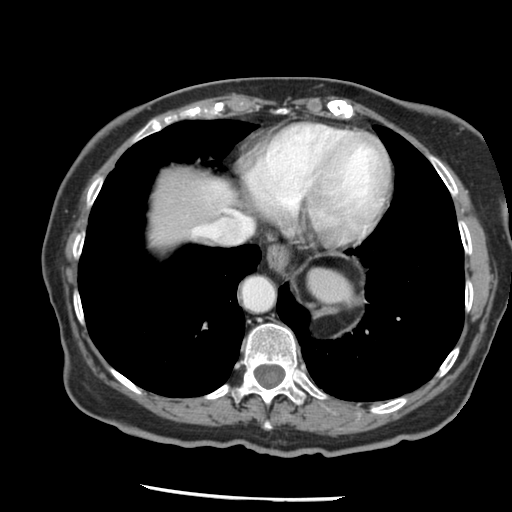
Contrast-enhanced abdominal CT, one axial slice; position 119 of 148 along the scan axis; soft-tissue window (W 400 / L 40 HU); 2.5 mm slice thickness; 512 × 512 image matrix, field of view 330 × 330 mm. Female patient, age 85 years. From the clinical record (not read from this slice): diagnosis: colorectal cancer liver metastases, imaged before liver resection; multiple liver metastases: no; largest metastasis: 0.9 cm; chemotherapy before resection: yes.
Outlined on this slice (outlined manually by an expert reader):
- hepatic veins: box from (x=192, y=210) to (x=252, y=244) px
- liver: (x=147, y=168)–(x=237, y=253)
- planned liver remnant (the part of the liver to remain after resection): (x=147, y=168)–(x=237, y=253)